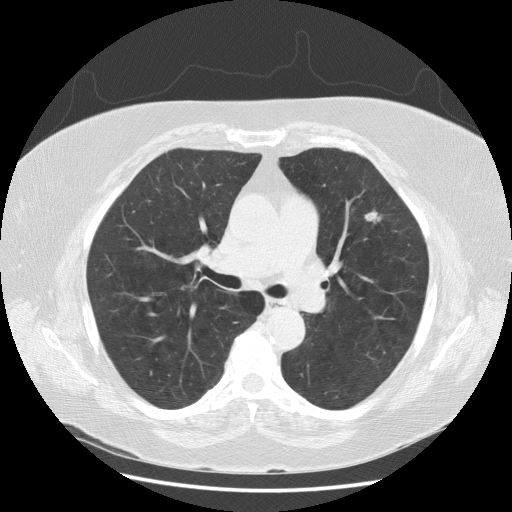
Axial slice from a low-dose chest CT screening exam; second annual screen; lung window (W 1500 / L -600 HU); standard (soft-tissue) reconstruction kernel (STANDARD); slice 66 of 164 in the series. Female participant, aged 68 years at enrolment. Current smoker at enrolment.
Expert reader's lesion annotation, bounding box [x1, y1, x2, y2] px = [360, 198, 399, 234]. The screening reader recorded 2 non-calcified nodules or masses ≥4 mm on this exam; which of them this box marks is not recorded. Official screen result: positive, other. Participant outcome: lung cancer diagnosed 90 days after this screen — large cell carcinoma, NOS, left upper lobe, undifferentiated (G4), stage IA (AJCC 6th edition), 10 mm at pathology.